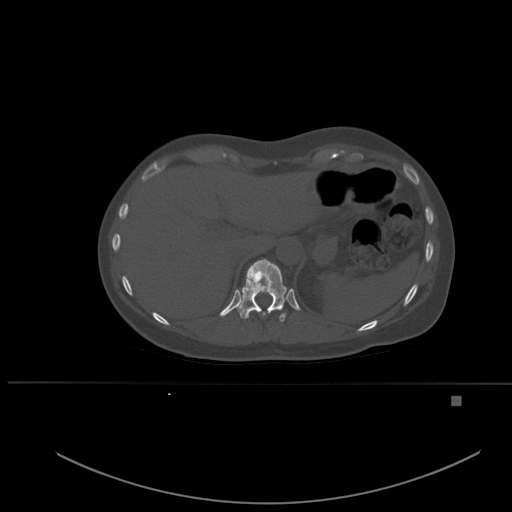
CT including the spine, one axial slice; position 276 of 651 along the scan axis; bone window (W 1800 / L 400 HU); 512 × 512 image matrix, field of view 443 × 443 mm. Female patient, age 49 years. Case-level facts recorded for this patient, not image findings: primary cancer: breast; vertebrae with lytic lesions (as recorded): L3, T12, L4.
Outlined on this slice (semi-automatic segmentation, software-assisted and operator-edited):
- T10 vertebra: bounding box (x1, y1, x2, y2) in pixels: (281, 308, 283, 315)
- T11 vertebra: (237, 259, 287, 322)